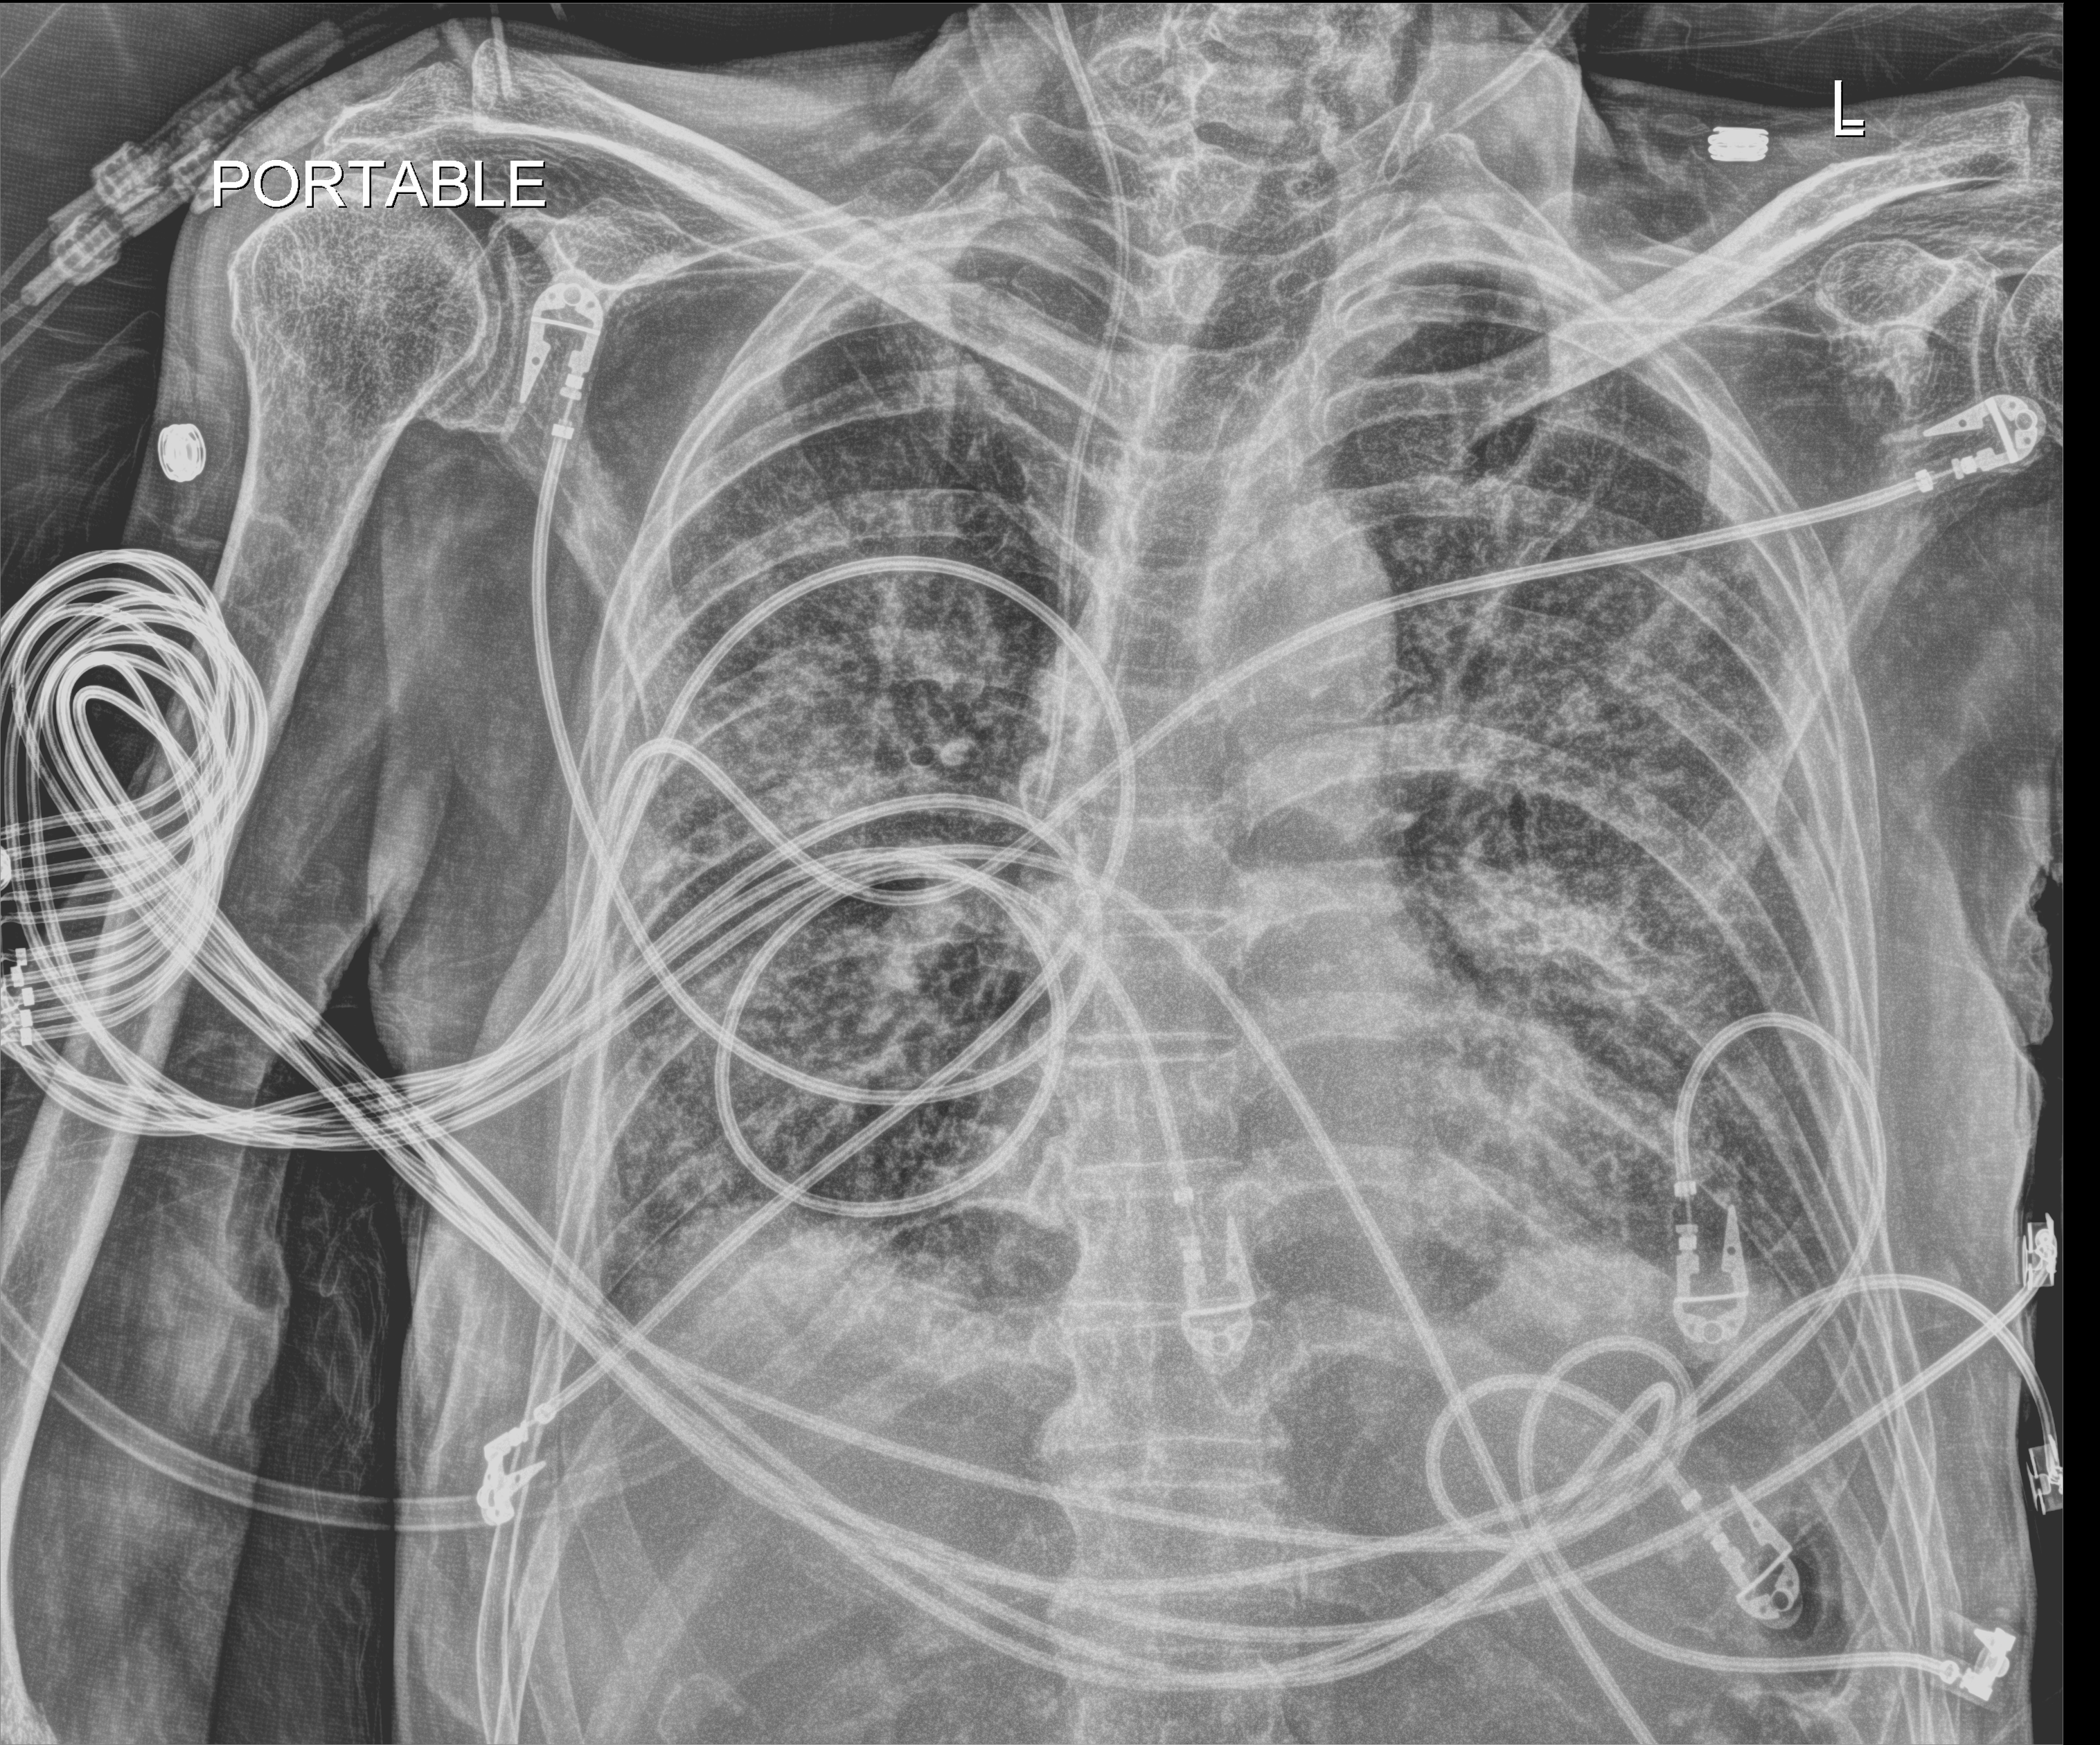
Bedside chest radiograph (digital radiography); anteroposterior (AP) projection. Male patient hospitalised with COVID-19, age 60–74 years.
From the hospital-stay record, not from the radiograph (when in the stay this image was taken is not recorded): mechanically ventilated during this hospital stay: yes; length of hospital stay: 42 days.